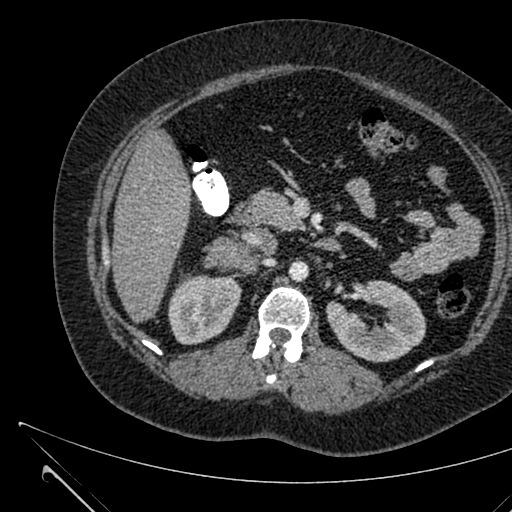
Contrast-enhanced abdominal CT, one axial slice. Position 355 of 731 along the scan axis. 120 kVp. Intravenous contrast given. Soft-tissue window (W 400 / L 40 HU). 1 mm slice thickness. 512 × 512 image matrix, field of view 376 × 376 mm. Female patient, age 36 years. Case-level facts recorded for this patient, not image findings: diagnosis: adrenocortical carcinoma; tumour side: right adrenal; tumour size at pathology: 10 cm; Ki-67 index: 20 %; stage (as recorded): 4.
Annotated regions visible in this slice (semi-automatic segmentation, software-assisted and operator-edited):
- mass: bounding box <206,236,250,269> (left, top, right, bottom; pixels)